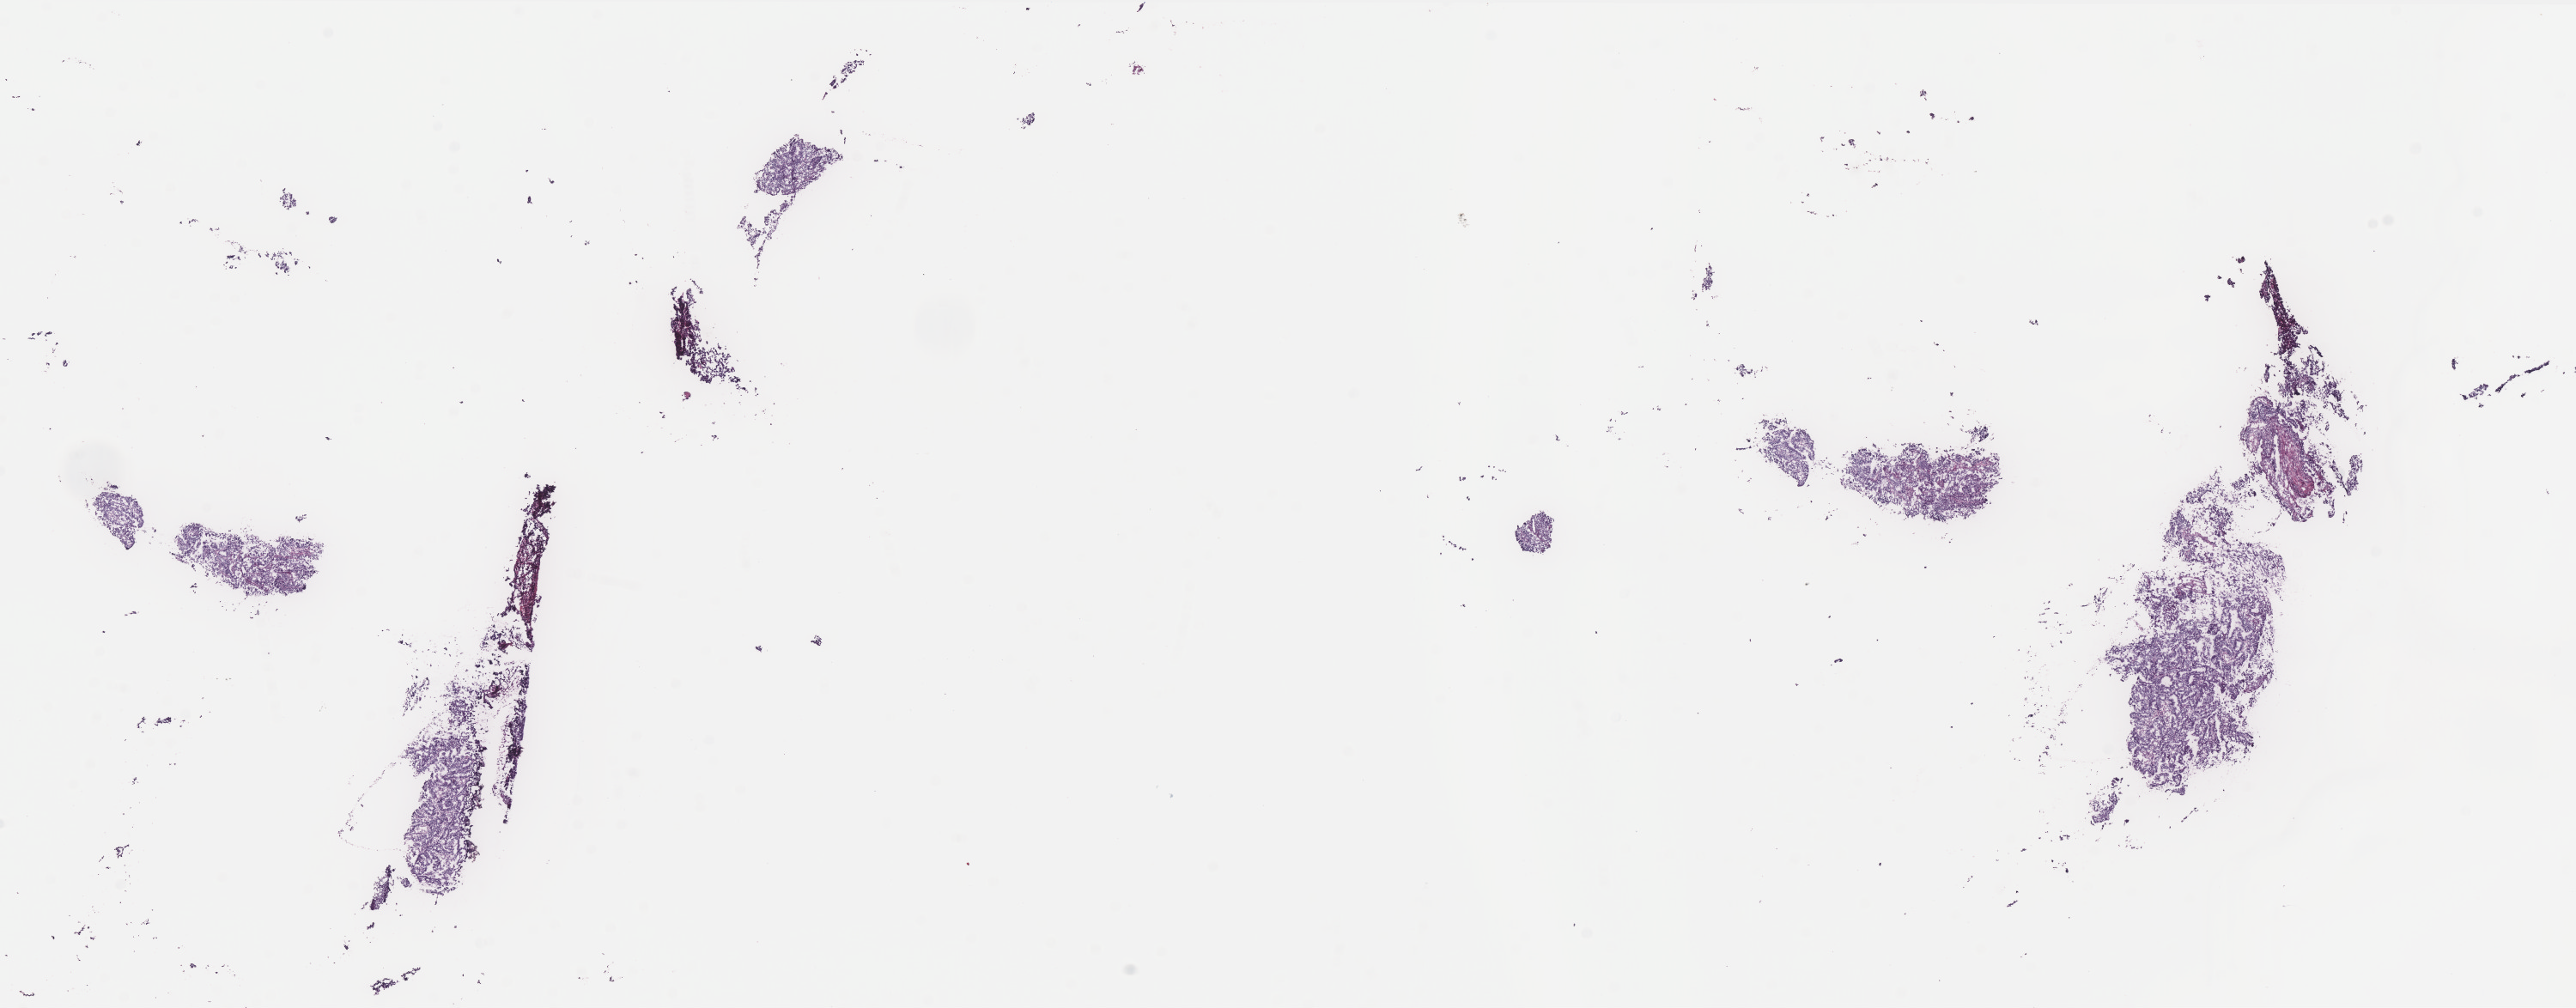
H&E-stained whole-slide image, whole scanned area (about 24.1 x 9.4 mm, acquisition: 40x scan) shown as a low-resolution overview, frozen section, sample: primary tumour, uterus. Patient: female, age at initial diagnosis 56 years. Histologic grade: G2 (moderately differentiated). Composition of this section per pathologist review: tumour cells 70%, tumour nuclei 70%, normal cells 0%, stromal cells 20%, necrosis 10%. Inflammatory infiltration, as recorded: lymphocyte infiltration 30%, monocyte infiltration 20%, neutrophil infiltration 40%.
- FIGO stage: IIIA
- histologic diagnosis: Endometrioid adenocarcinoma, NOS (endometrium)